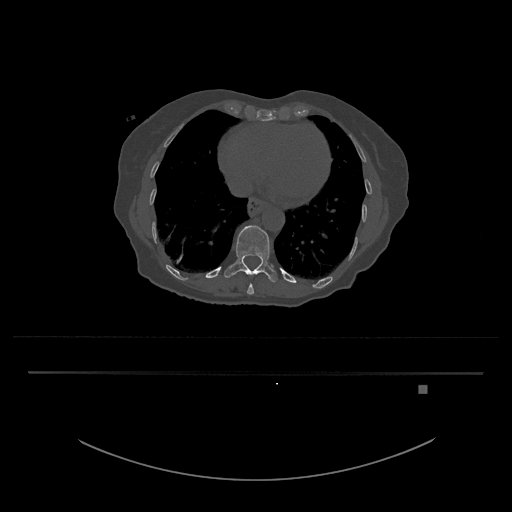
CT including the spine, one axial slice; reconstruction kernel Br40s/3; 120 kVp; bone window (W 1800 / L 400 HU); 512 × 512 image matrix, field of view 500 × 500 mm. Patient: female, 57 years. From the clinical record (not read from this slice): primary cancer: cervical.
Structures marked on this image (semi-automatic segmentation, software-assisted and operator-edited):
- T10 vertebra: box from (x=247, y=274) to (x=255, y=295) px
- T11 vertebra: (x=224, y=225)–(x=278, y=282)